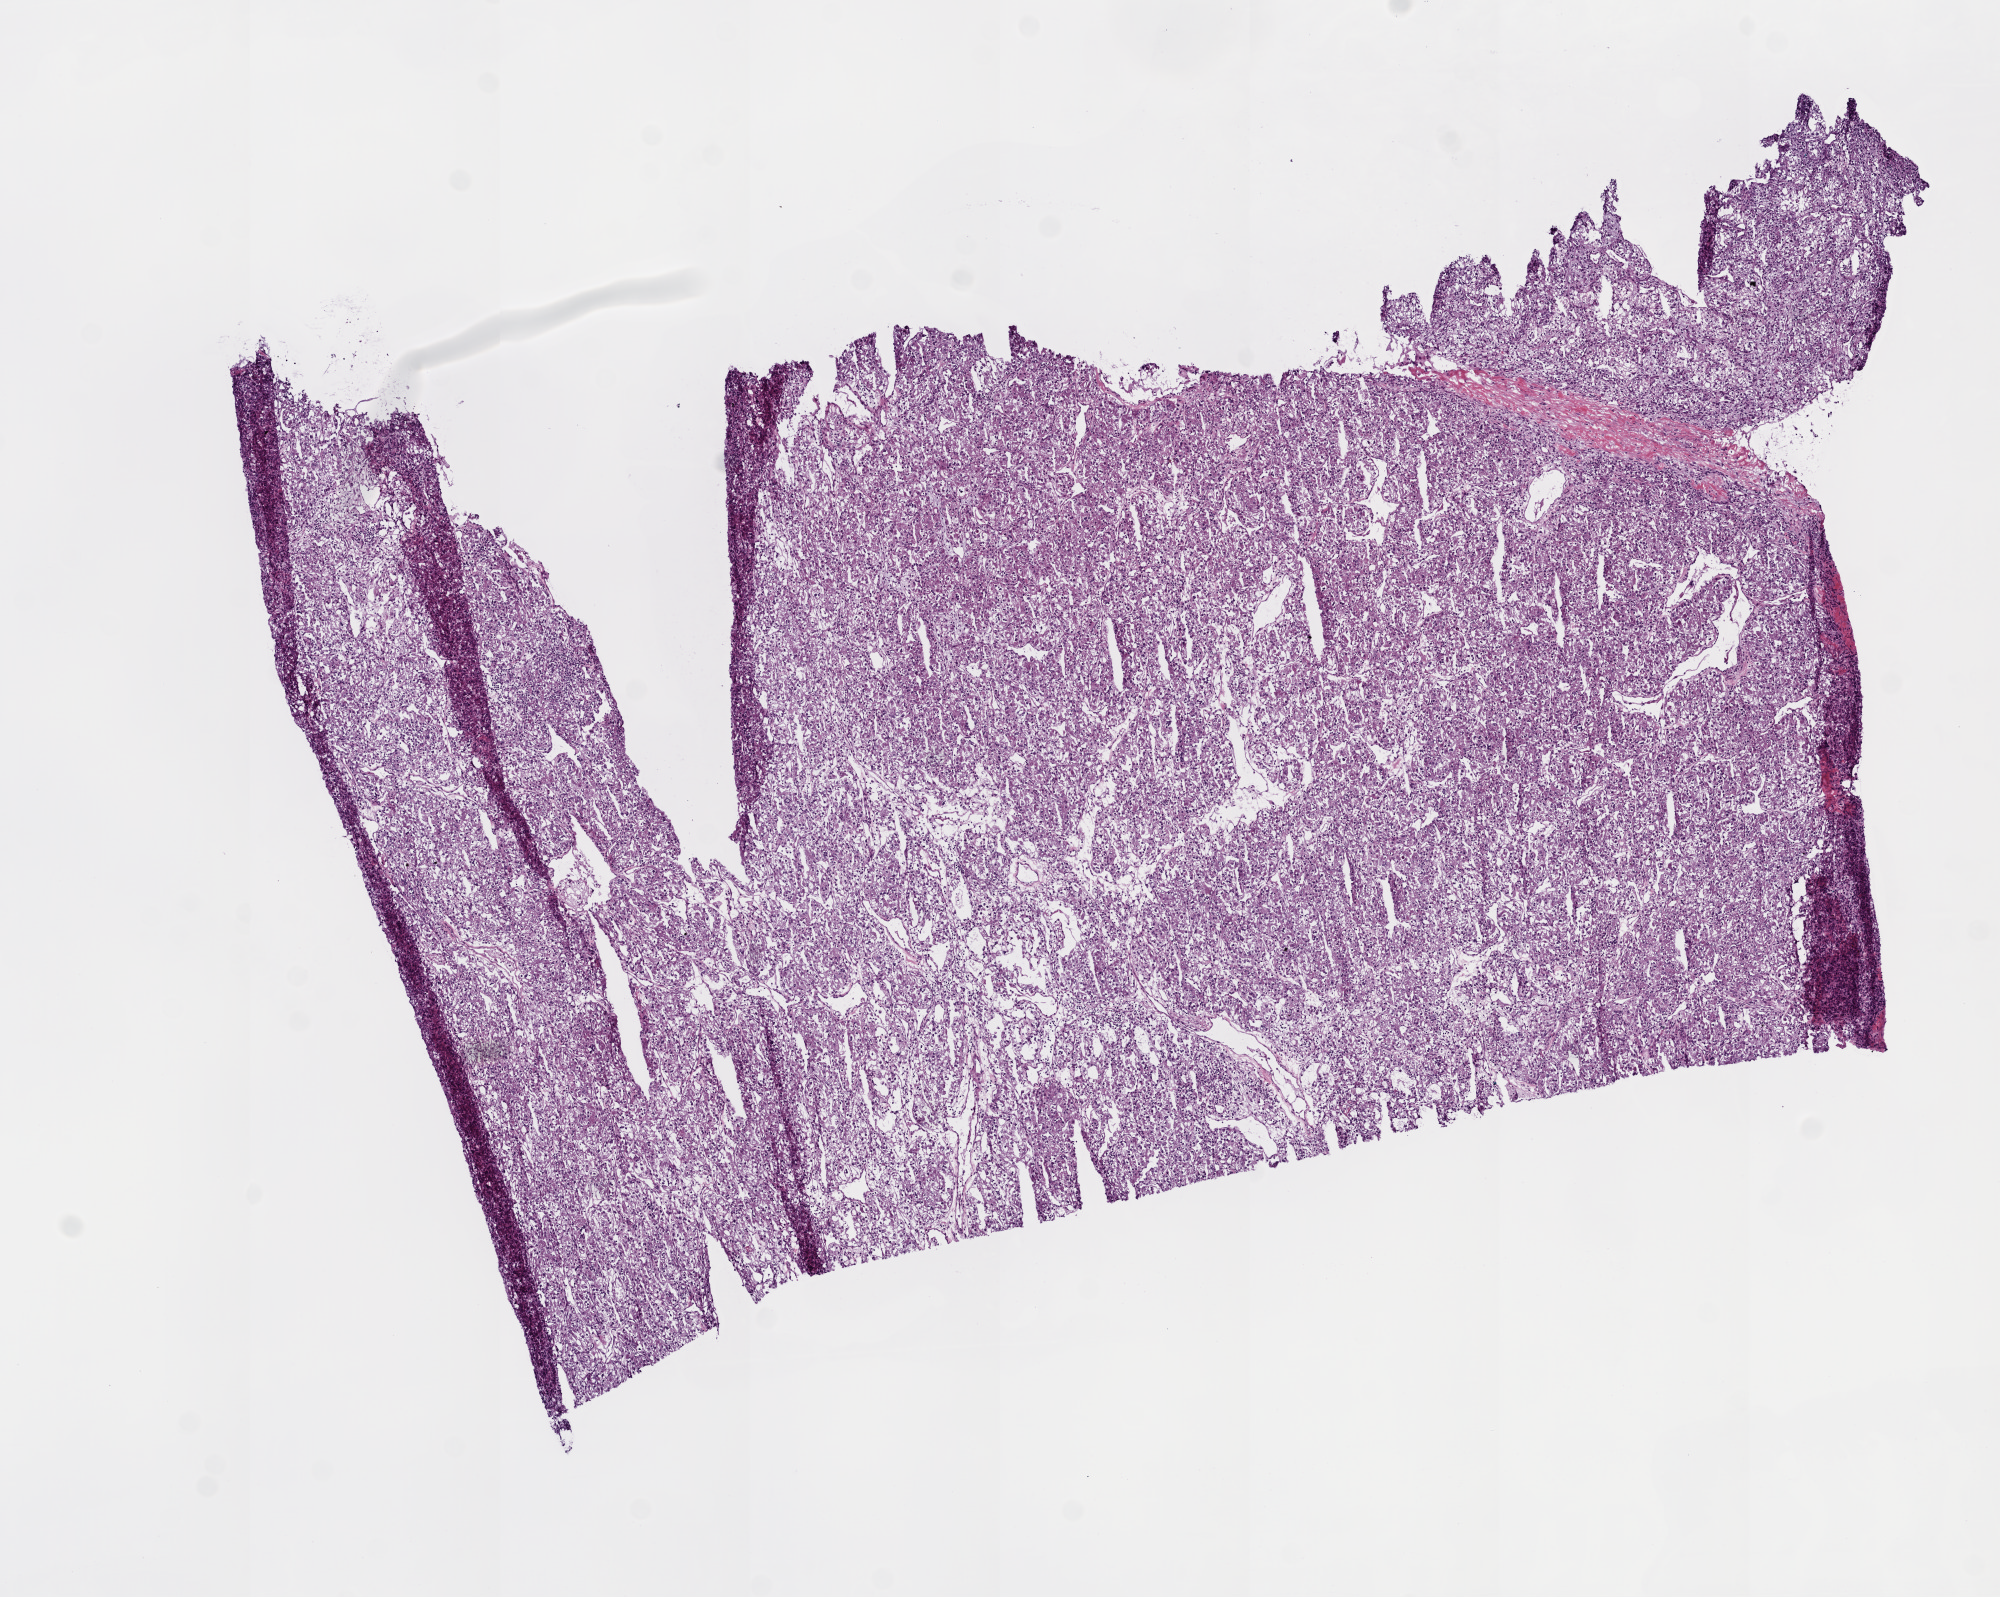
H&E whole-slide image, shown as a low-resolution overview of the whole scanned area (about 8.0 x 6.4 mm, slide scanned at 20x); frozen section from the top of the tissue portion; kidney, primary tumour sample. Male, age 51 years at initial diagnosis. Histologic grade: G3 (poorly differentiated). Pathologist review of this section (percent, as recorded): tumour cells 95%, tumour nuclei 90%, normal cells 0%, stromal cells 5%, necrosis 0%. Infiltration values recorded for this section: lymphocyte infiltration 3%, monocyte infiltration 1%, neutrophil infiltration 0%.
AJCC pathologic stage: IV. TNM: T3a NX M1. Pathologic diagnosis: Clear cell adenocarcinoma, NOS.